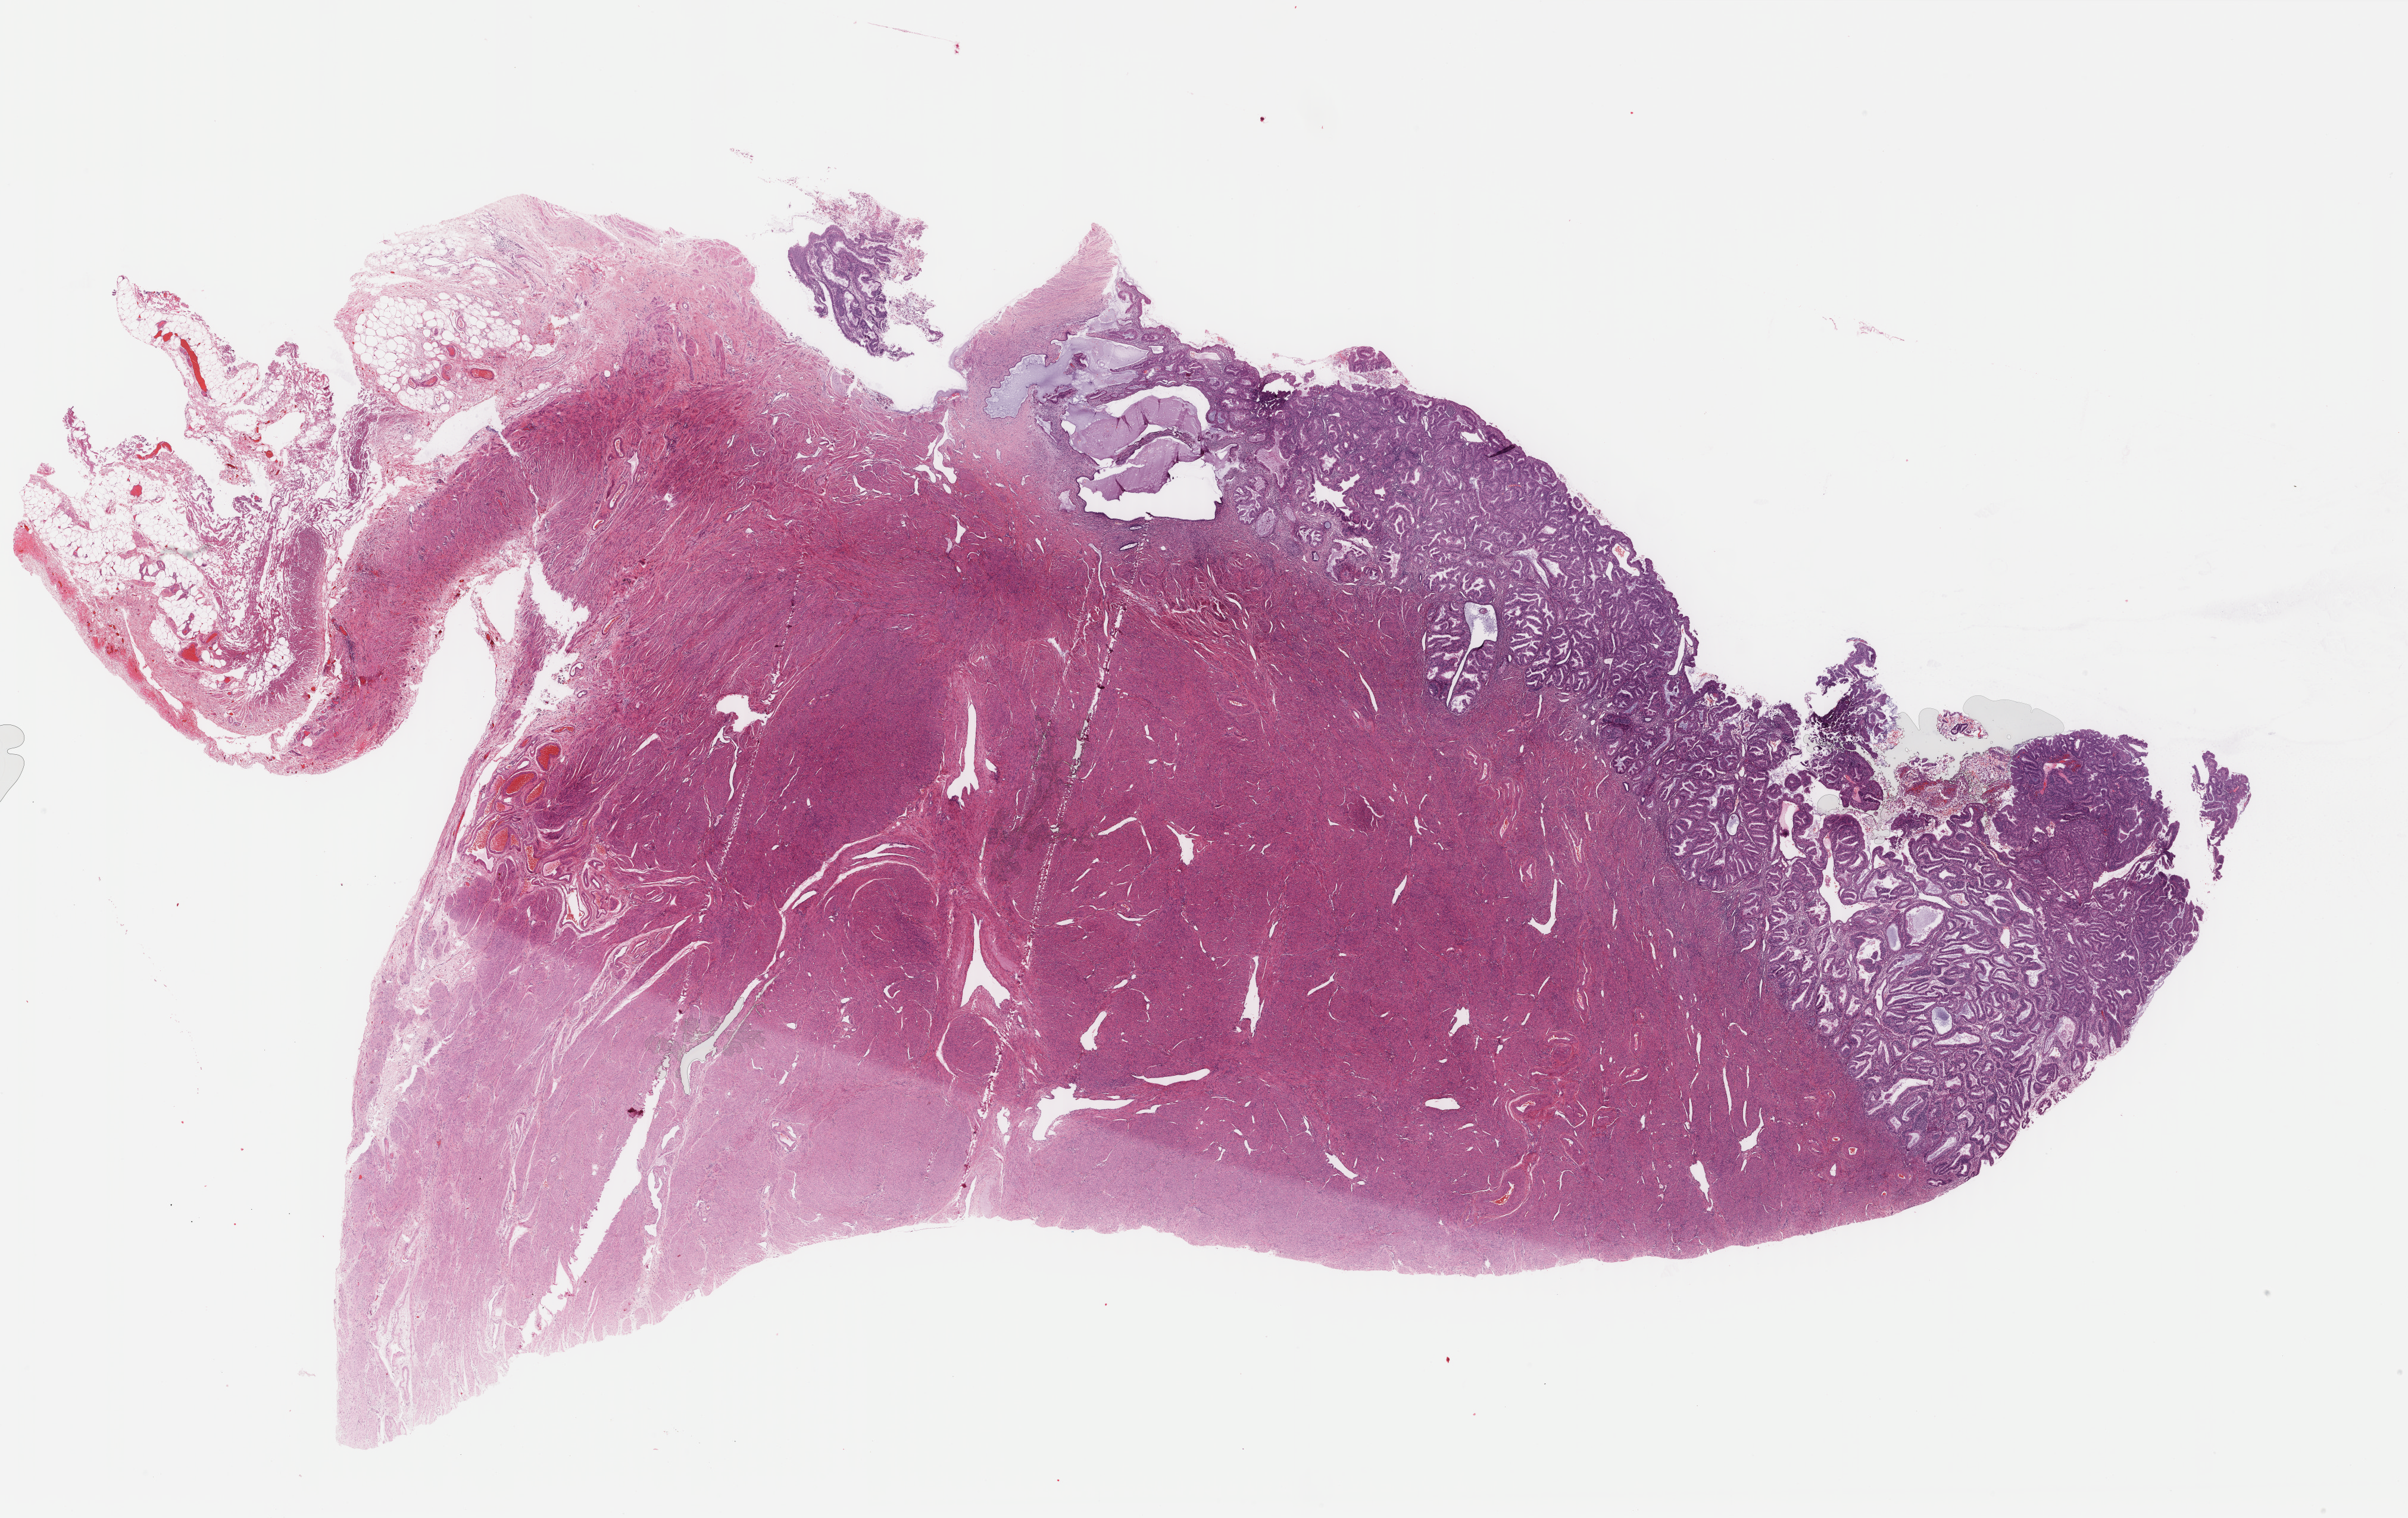
Digitized H&E-stained tissue section (whole slide), low-resolution overview of the scanned area, about 32.1 x 20.2 mm (from a 40x scan). Formalin-fixed paraffin-embedded (FFPE) diagnostic section. Uterus, primary tumour sample. Female, age 53 years at initial diagnosis. Histologic grade: G1 (well differentiated).
* FIGO stage: IA
* diagnosis: Endometrioid adenocarcinoma, NOS (endometrium)